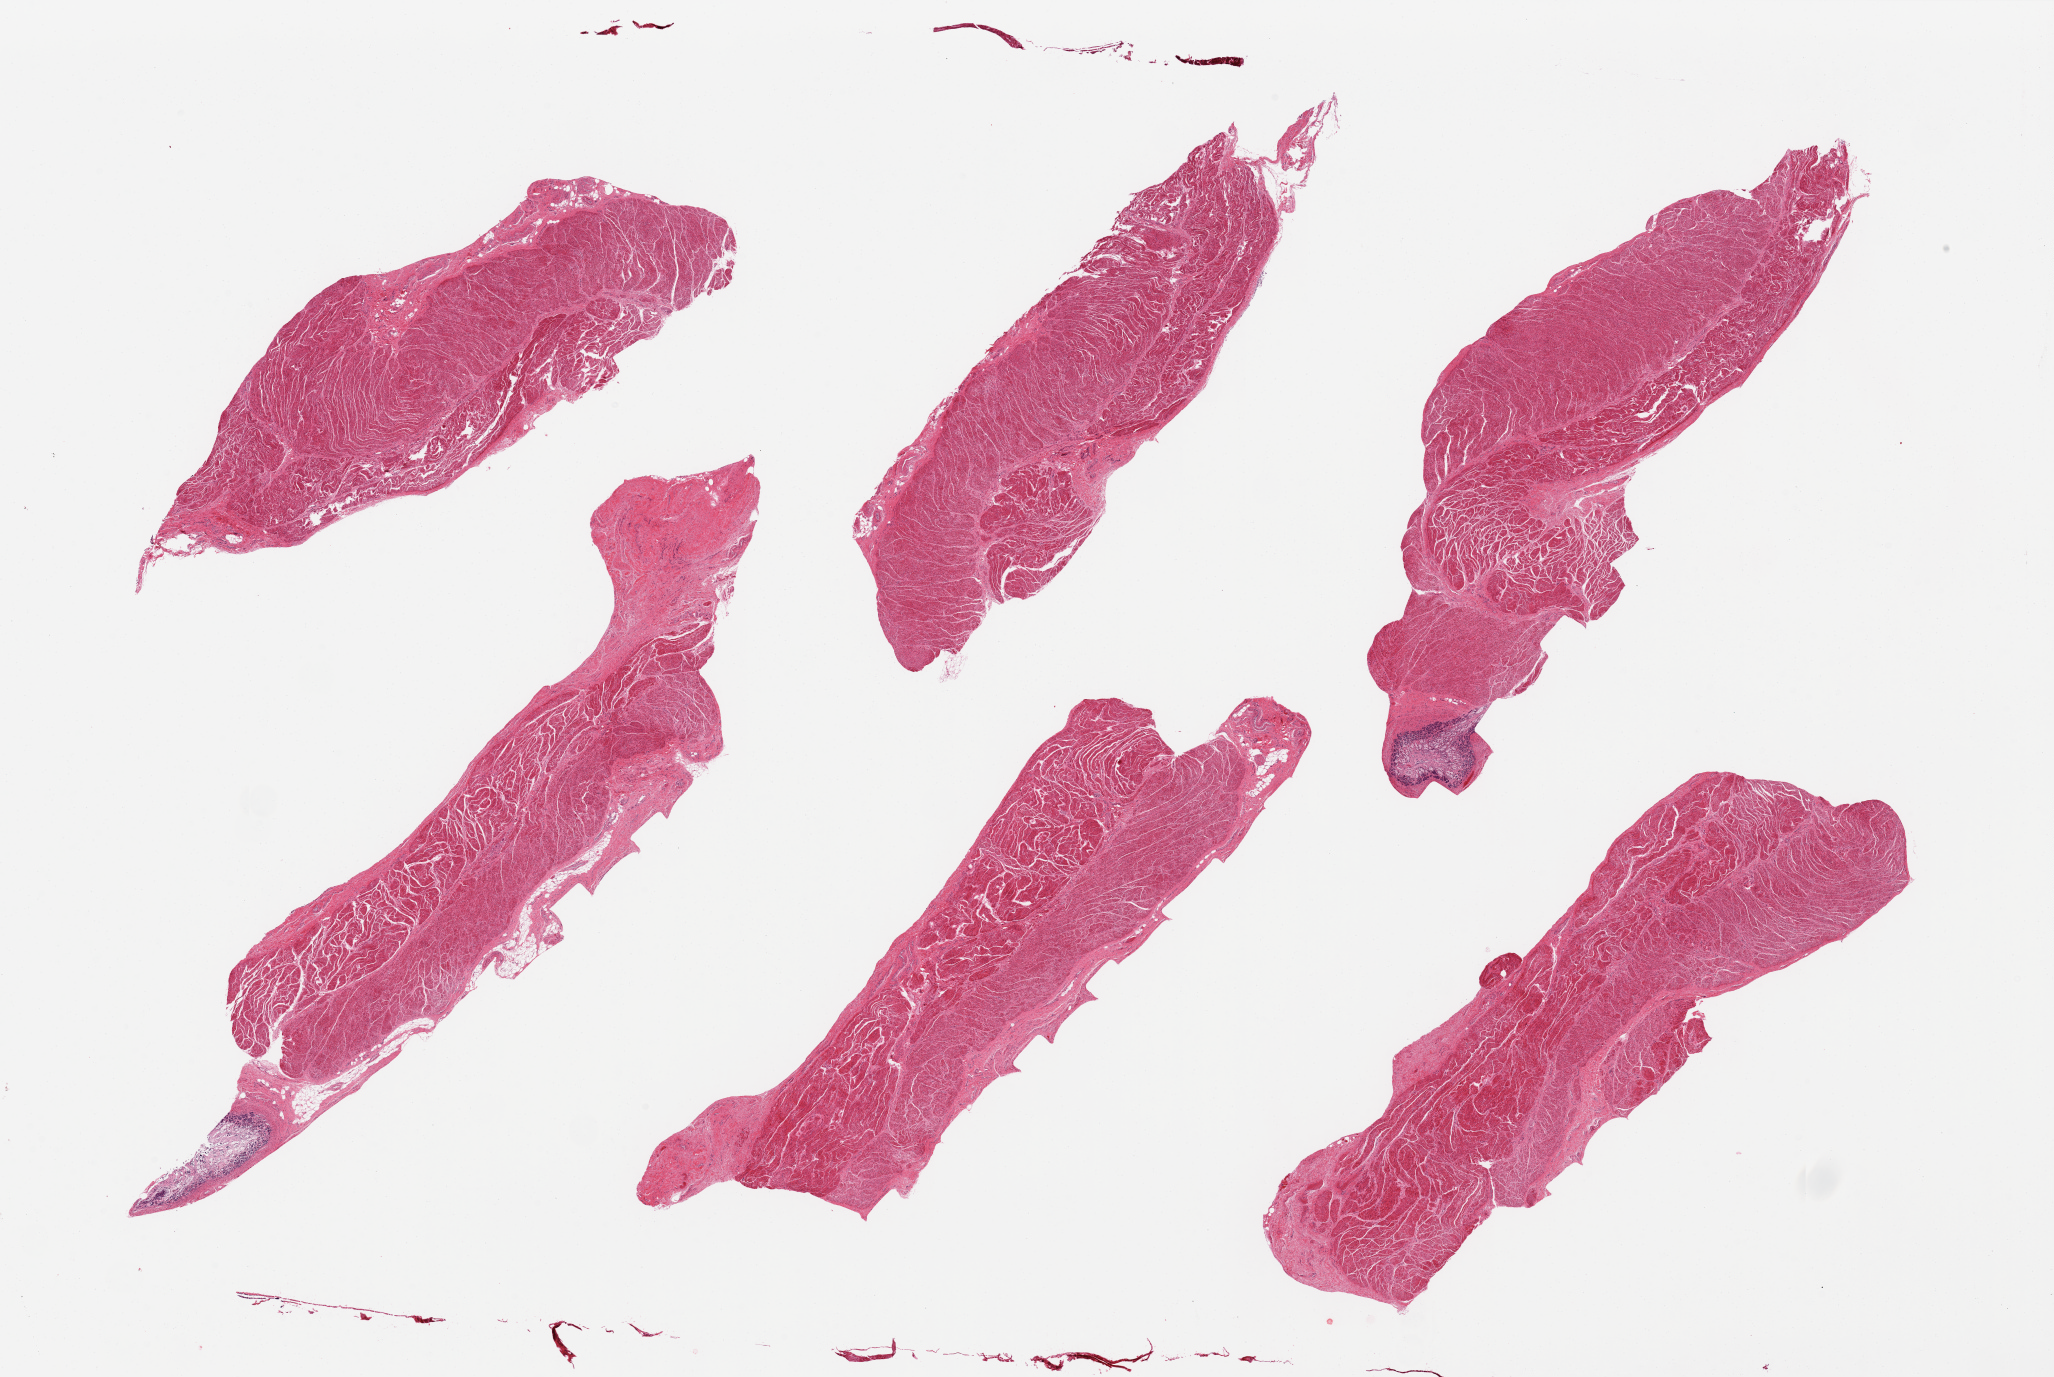
Digitized hematoxylin and eosin (H&E)-stained section, whole scanned area (about 32.5 x 21.8 mm, from a 20x scan) shown as a low-resolution overview; PAXgene-fixed paraffin-embedded (PFPE) section; target tissue: gastroesophageal junction; tissue donor sample.
Review note (as recorded): 6 pieces, predominantly muscularis, but two pieces include portion of markedly autolyzed gastric mucosa (not target/preferred location).